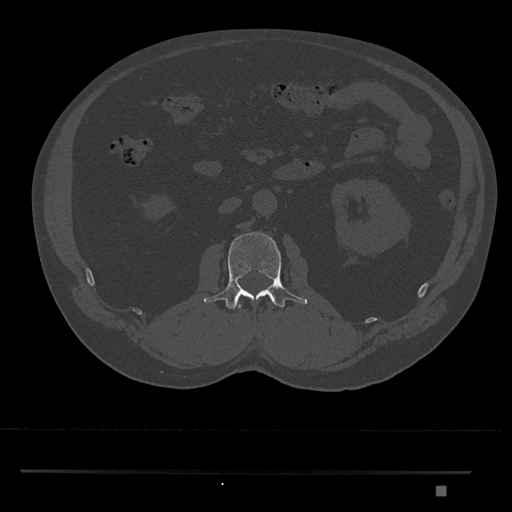
CT including the spine, one axial slice. Slice 759 of 1134 in the series (ordered by position). Bone window (W 1800 / L 400 HU). 0.5 mm slice thickness. 512 × 512 image matrix, field of view 429 × 429 mm. Male patient, age 65 years. From the clinical record (not read from this slice): primary cancer: prostate.
Outlined on this slice (semi-automatic segmentation, software-assisted and operator-edited):
- L1 vertebra: bounding box [x1, y1, x2, y2] px = [238, 305, 242, 309]
- L2 vertebra: [204, 232, 308, 310]